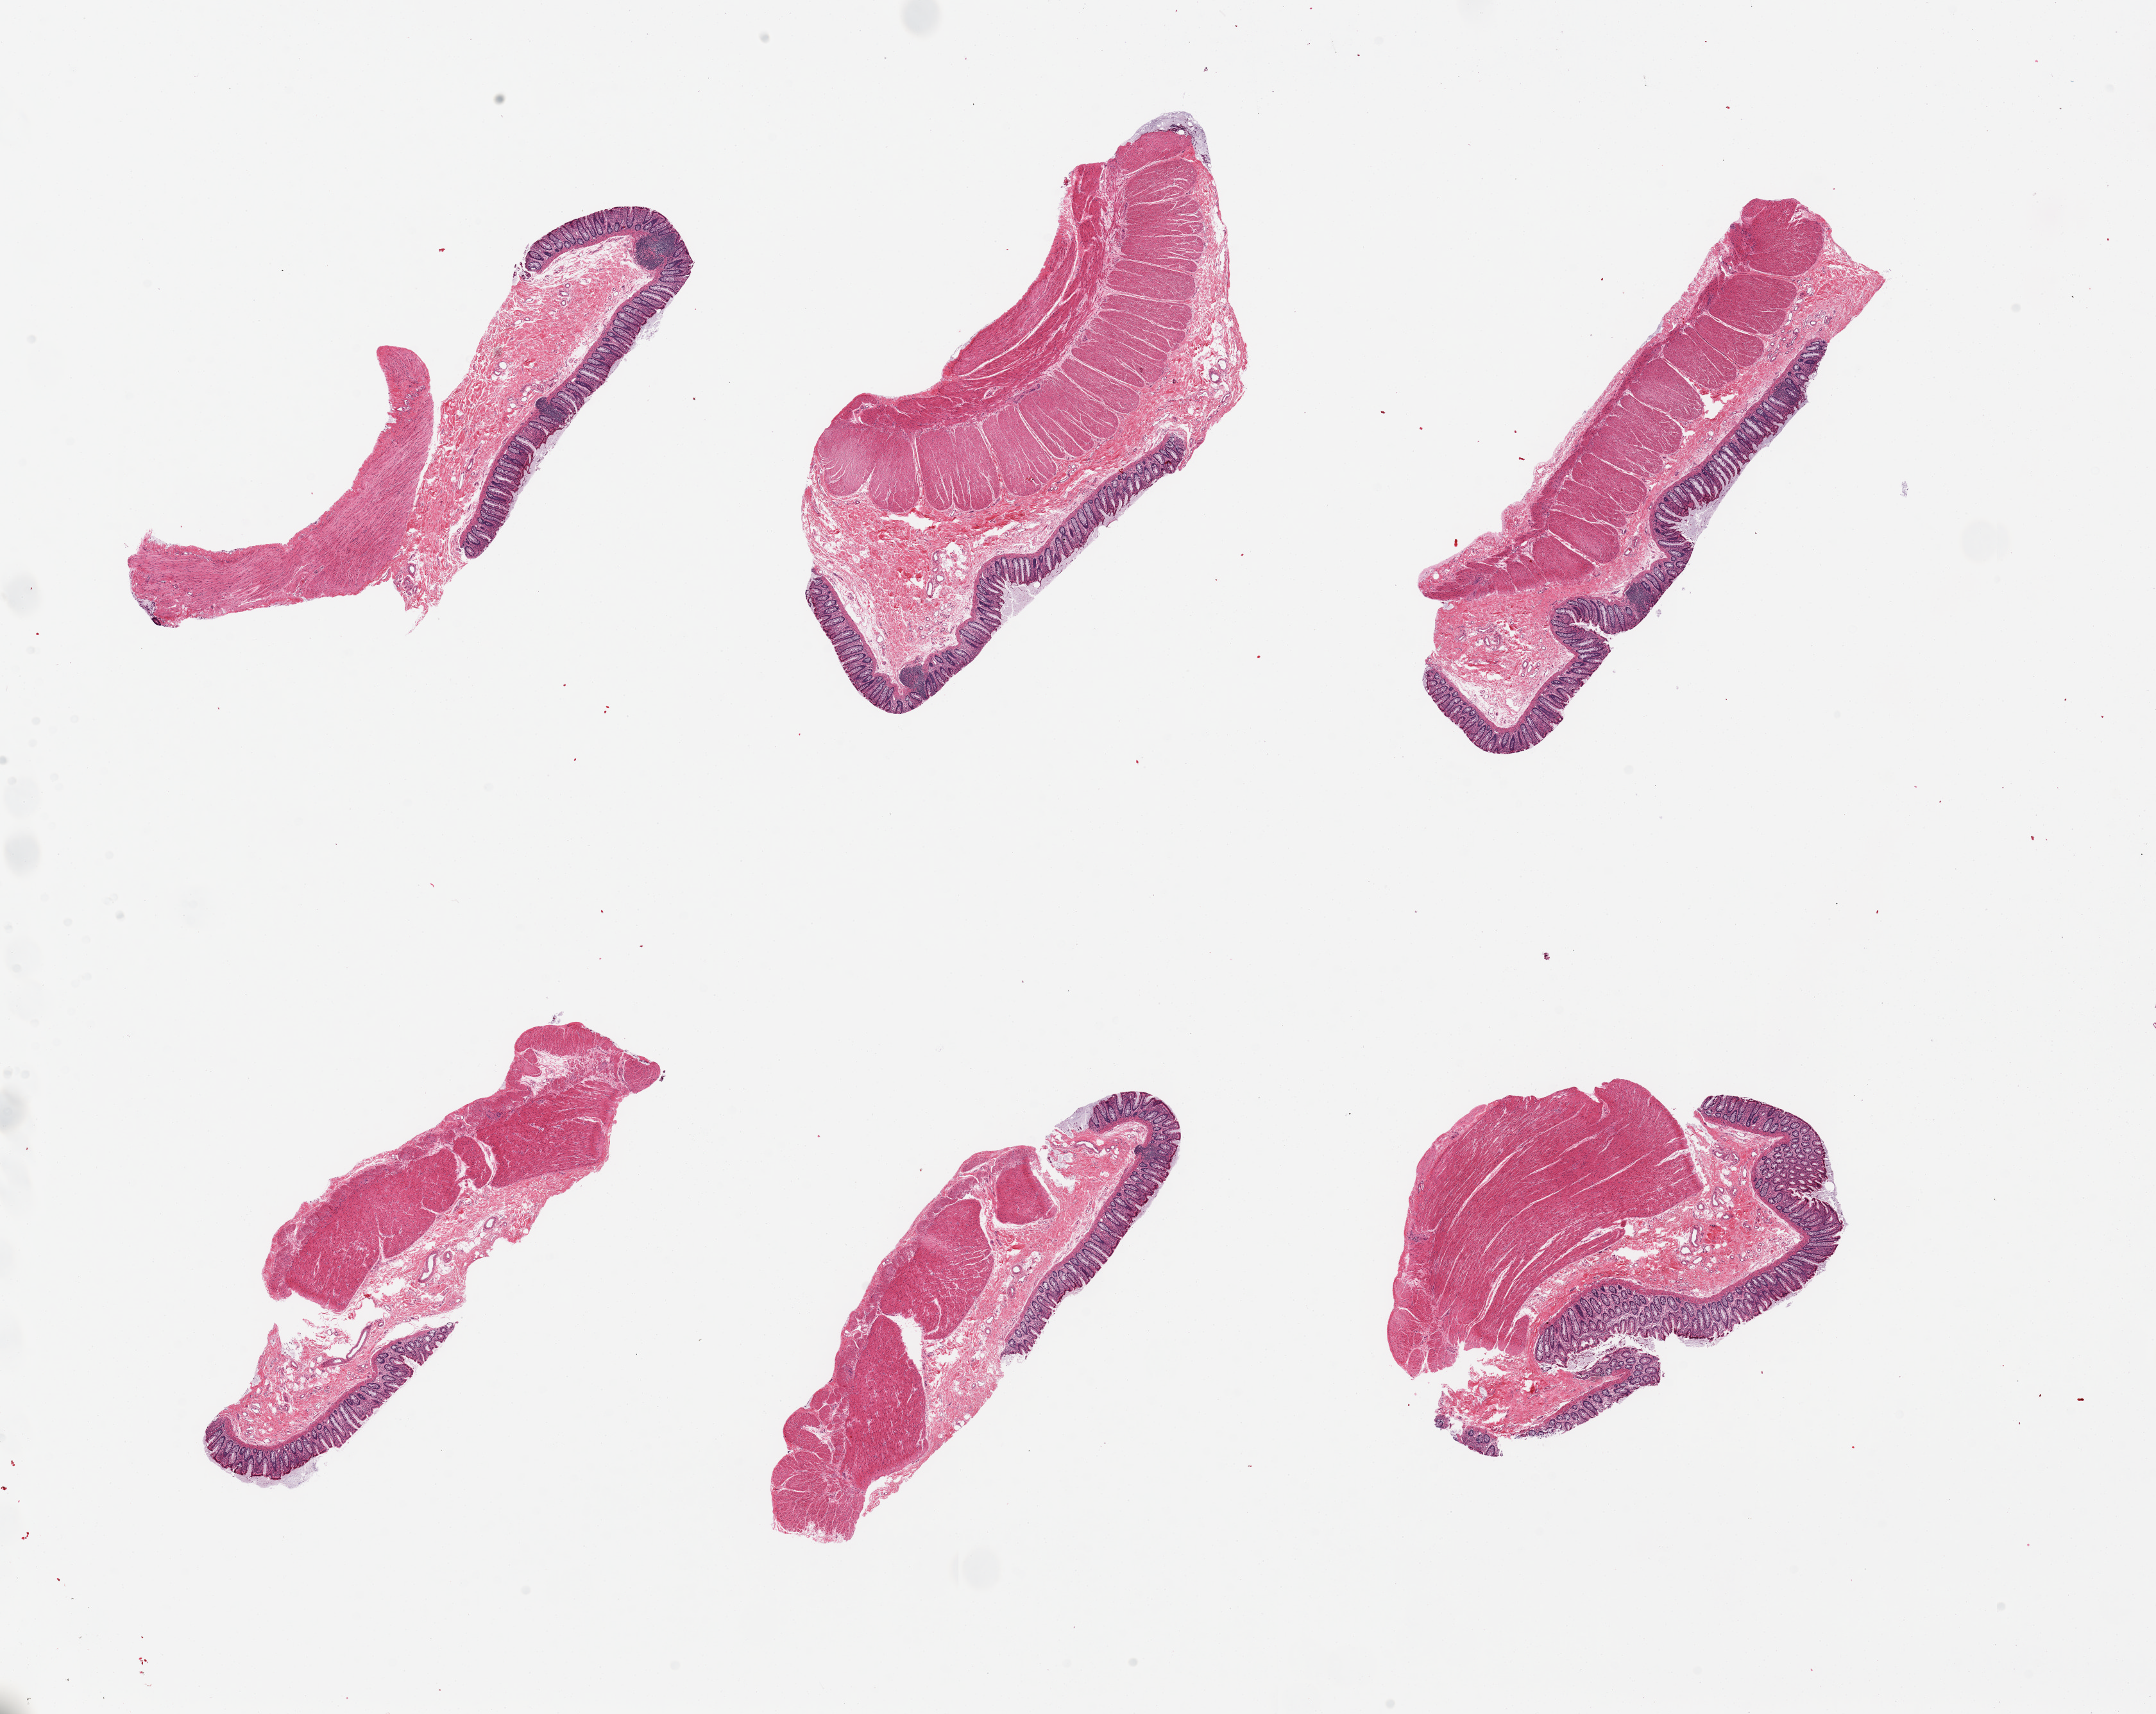
Digitized hematoxylin and eosin (H&E)-stained section, a low-resolution overview of the entire scanned area, about 26.6 x 21.1 mm (from a 20x scan), PAXgene-fixed, paraffin-embedded tissue, sampled site (target tissue): transverse colon, donor tissue sample. Donor sex: female.
Reviewer comment on this tissue sample: 6 pieces well dissected full thickness of colon.